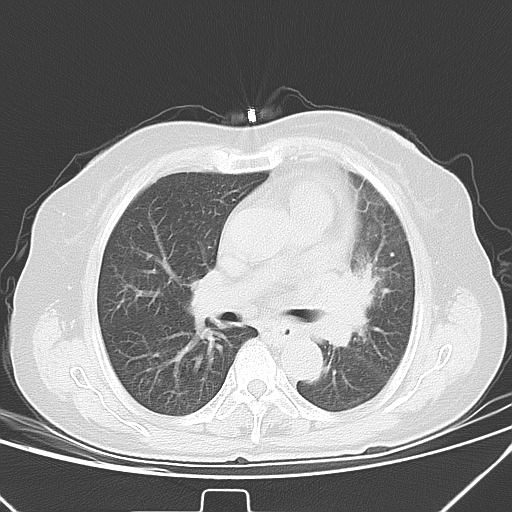
Chest CT, one axial slice. Slice 23 of 40 in the series (ordered by position). 120 kVp. Lung window (W 1500 / L -600 HU). 512 × 512 image matrix, field of view 331 × 331 mm. Patient: female, 59 years. From the clinical record (not read from this slice): clinical TNM (as recorded): T3 N1 M0; histopathological grade: G3.
Annotated regions visible in this slice (rectangle marked by the reading radiologist):
- lung tumour (recorded histology: small cell carcinoma): bounding box <328,266,384,359> (left, top, right, bottom; pixels)